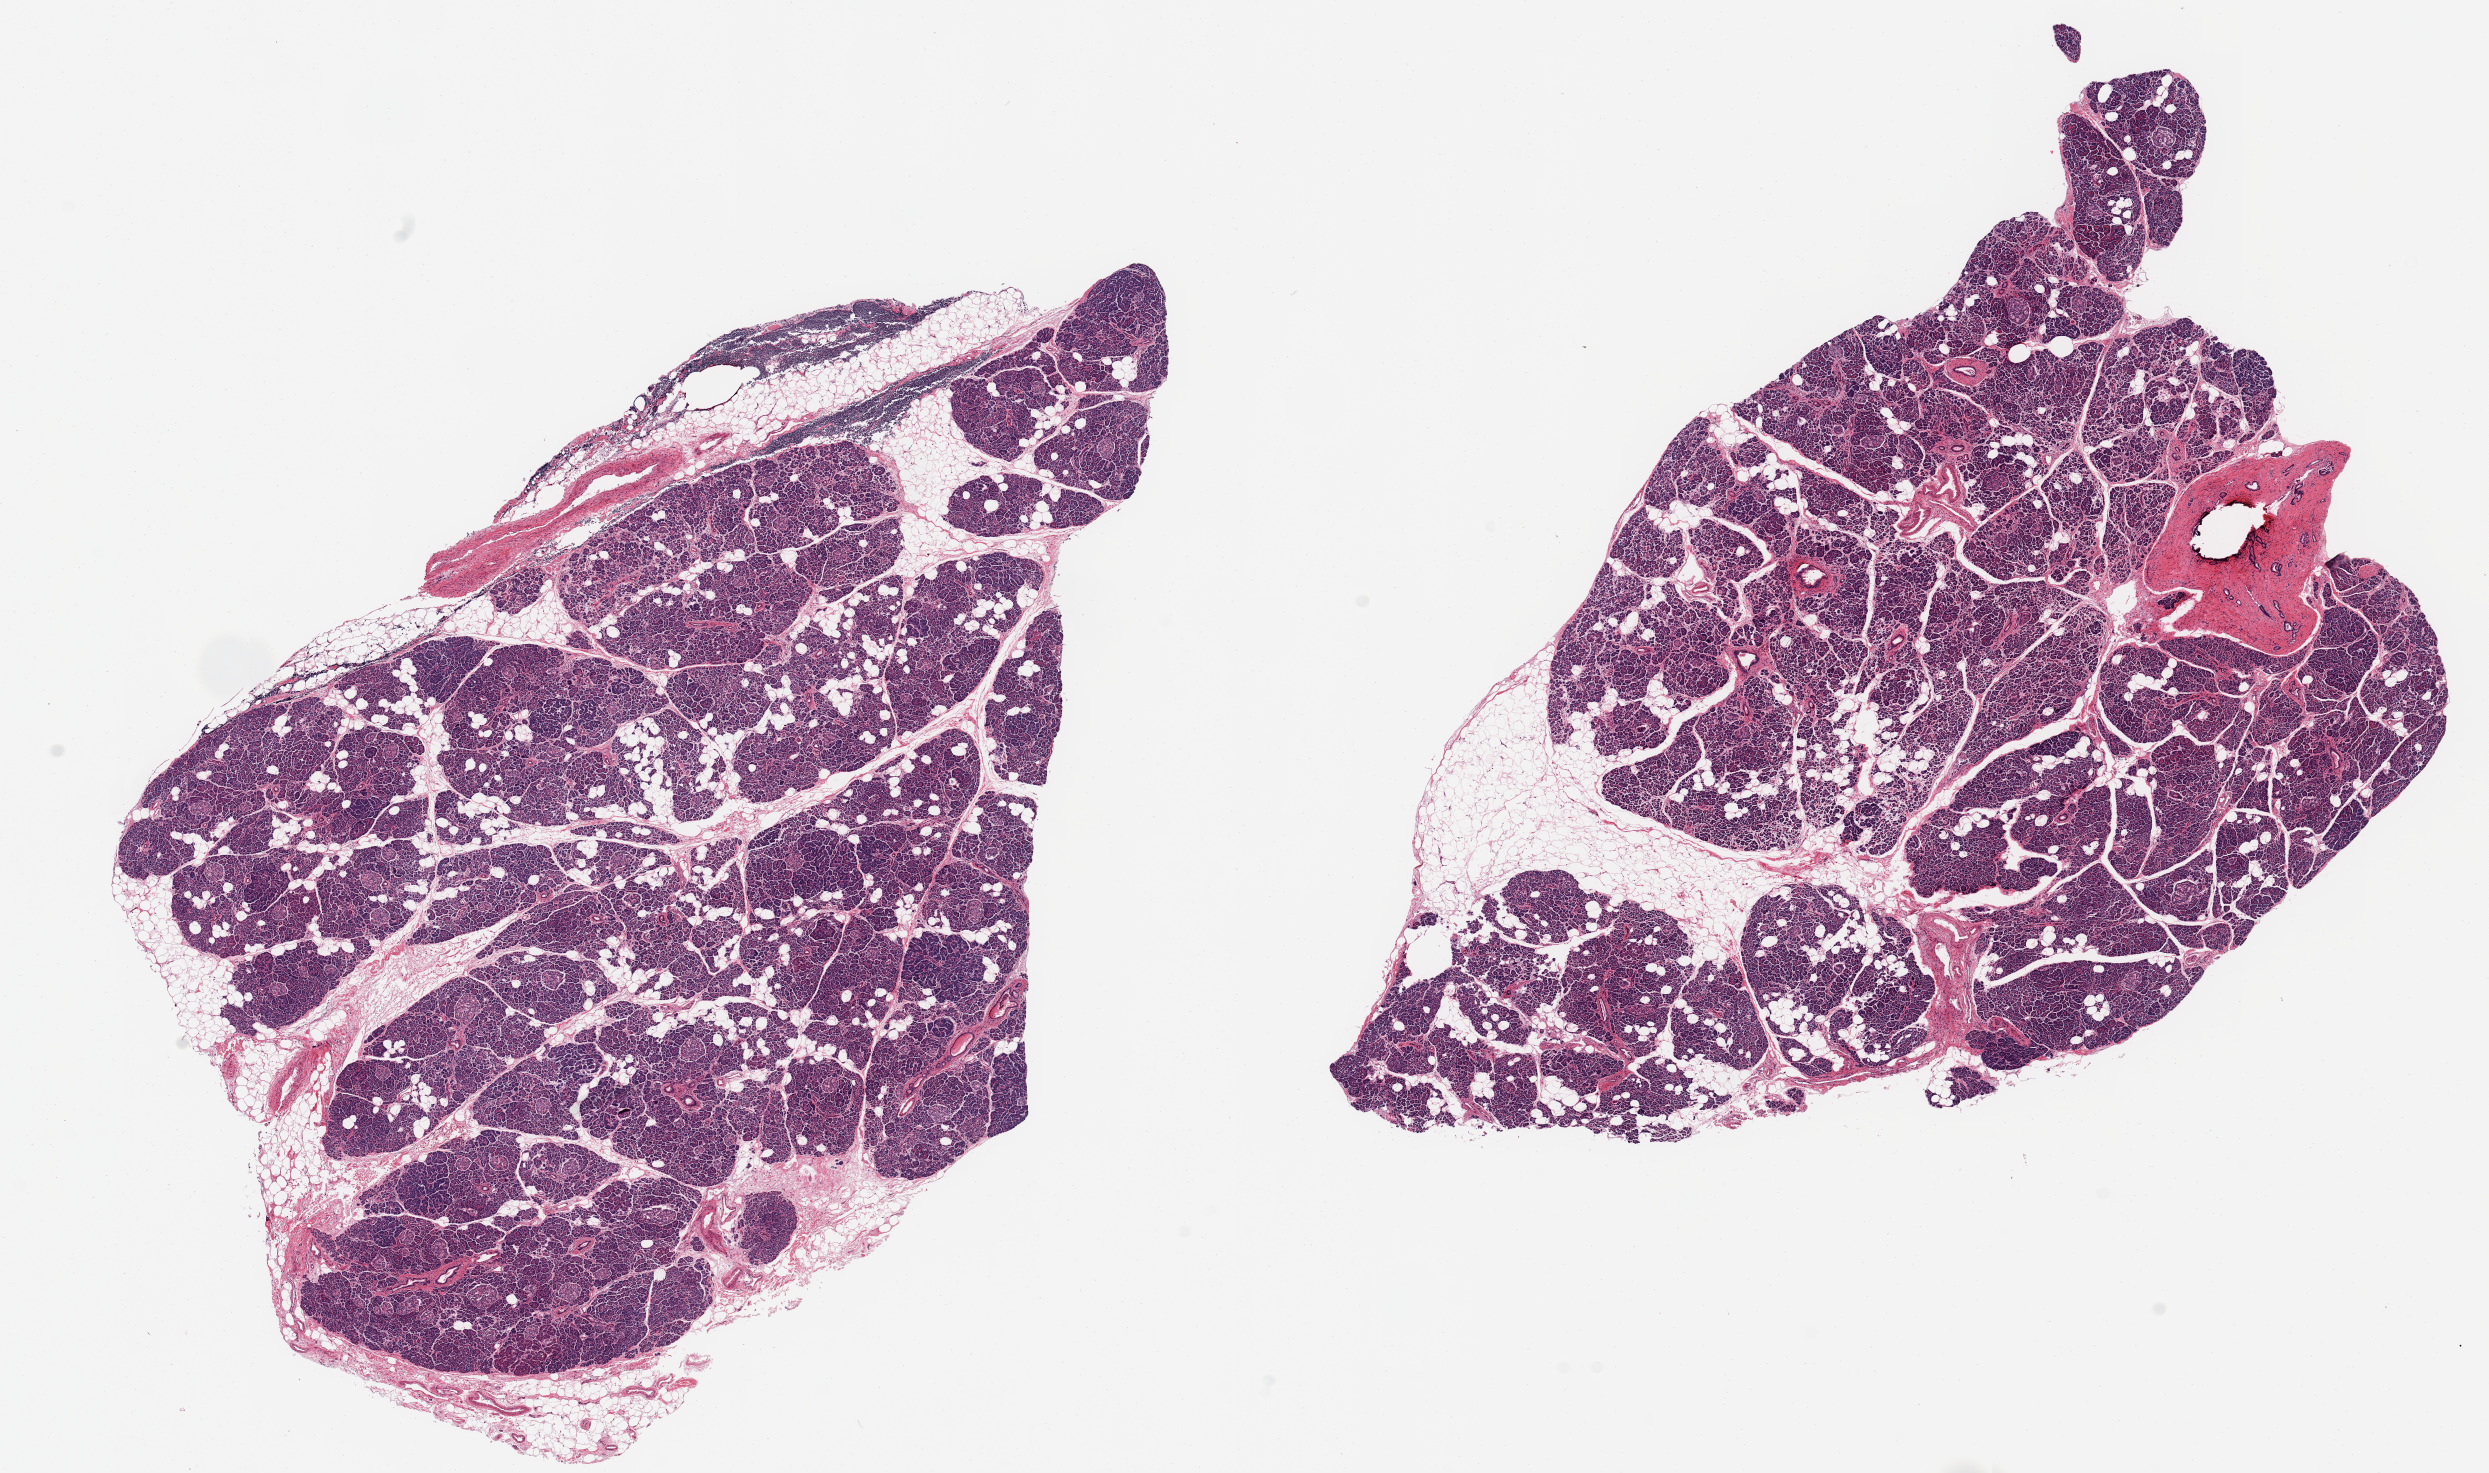
Digitized haematoxylin and eosin-stained section, low-resolution overview of the scanned area, about 19.7 x 11.7 mm (slide scanned at 20x). PAXgene-fixed paraffin-embedded (PFPE) section. Target tissue: pancreas. Tissue donor sample. Donor sex: female.
Pathologist's review note for this sample: 2 pieces; includes about 20-30% internal and external fat, lymphoid aggregate, islets are numerous/well visualized.